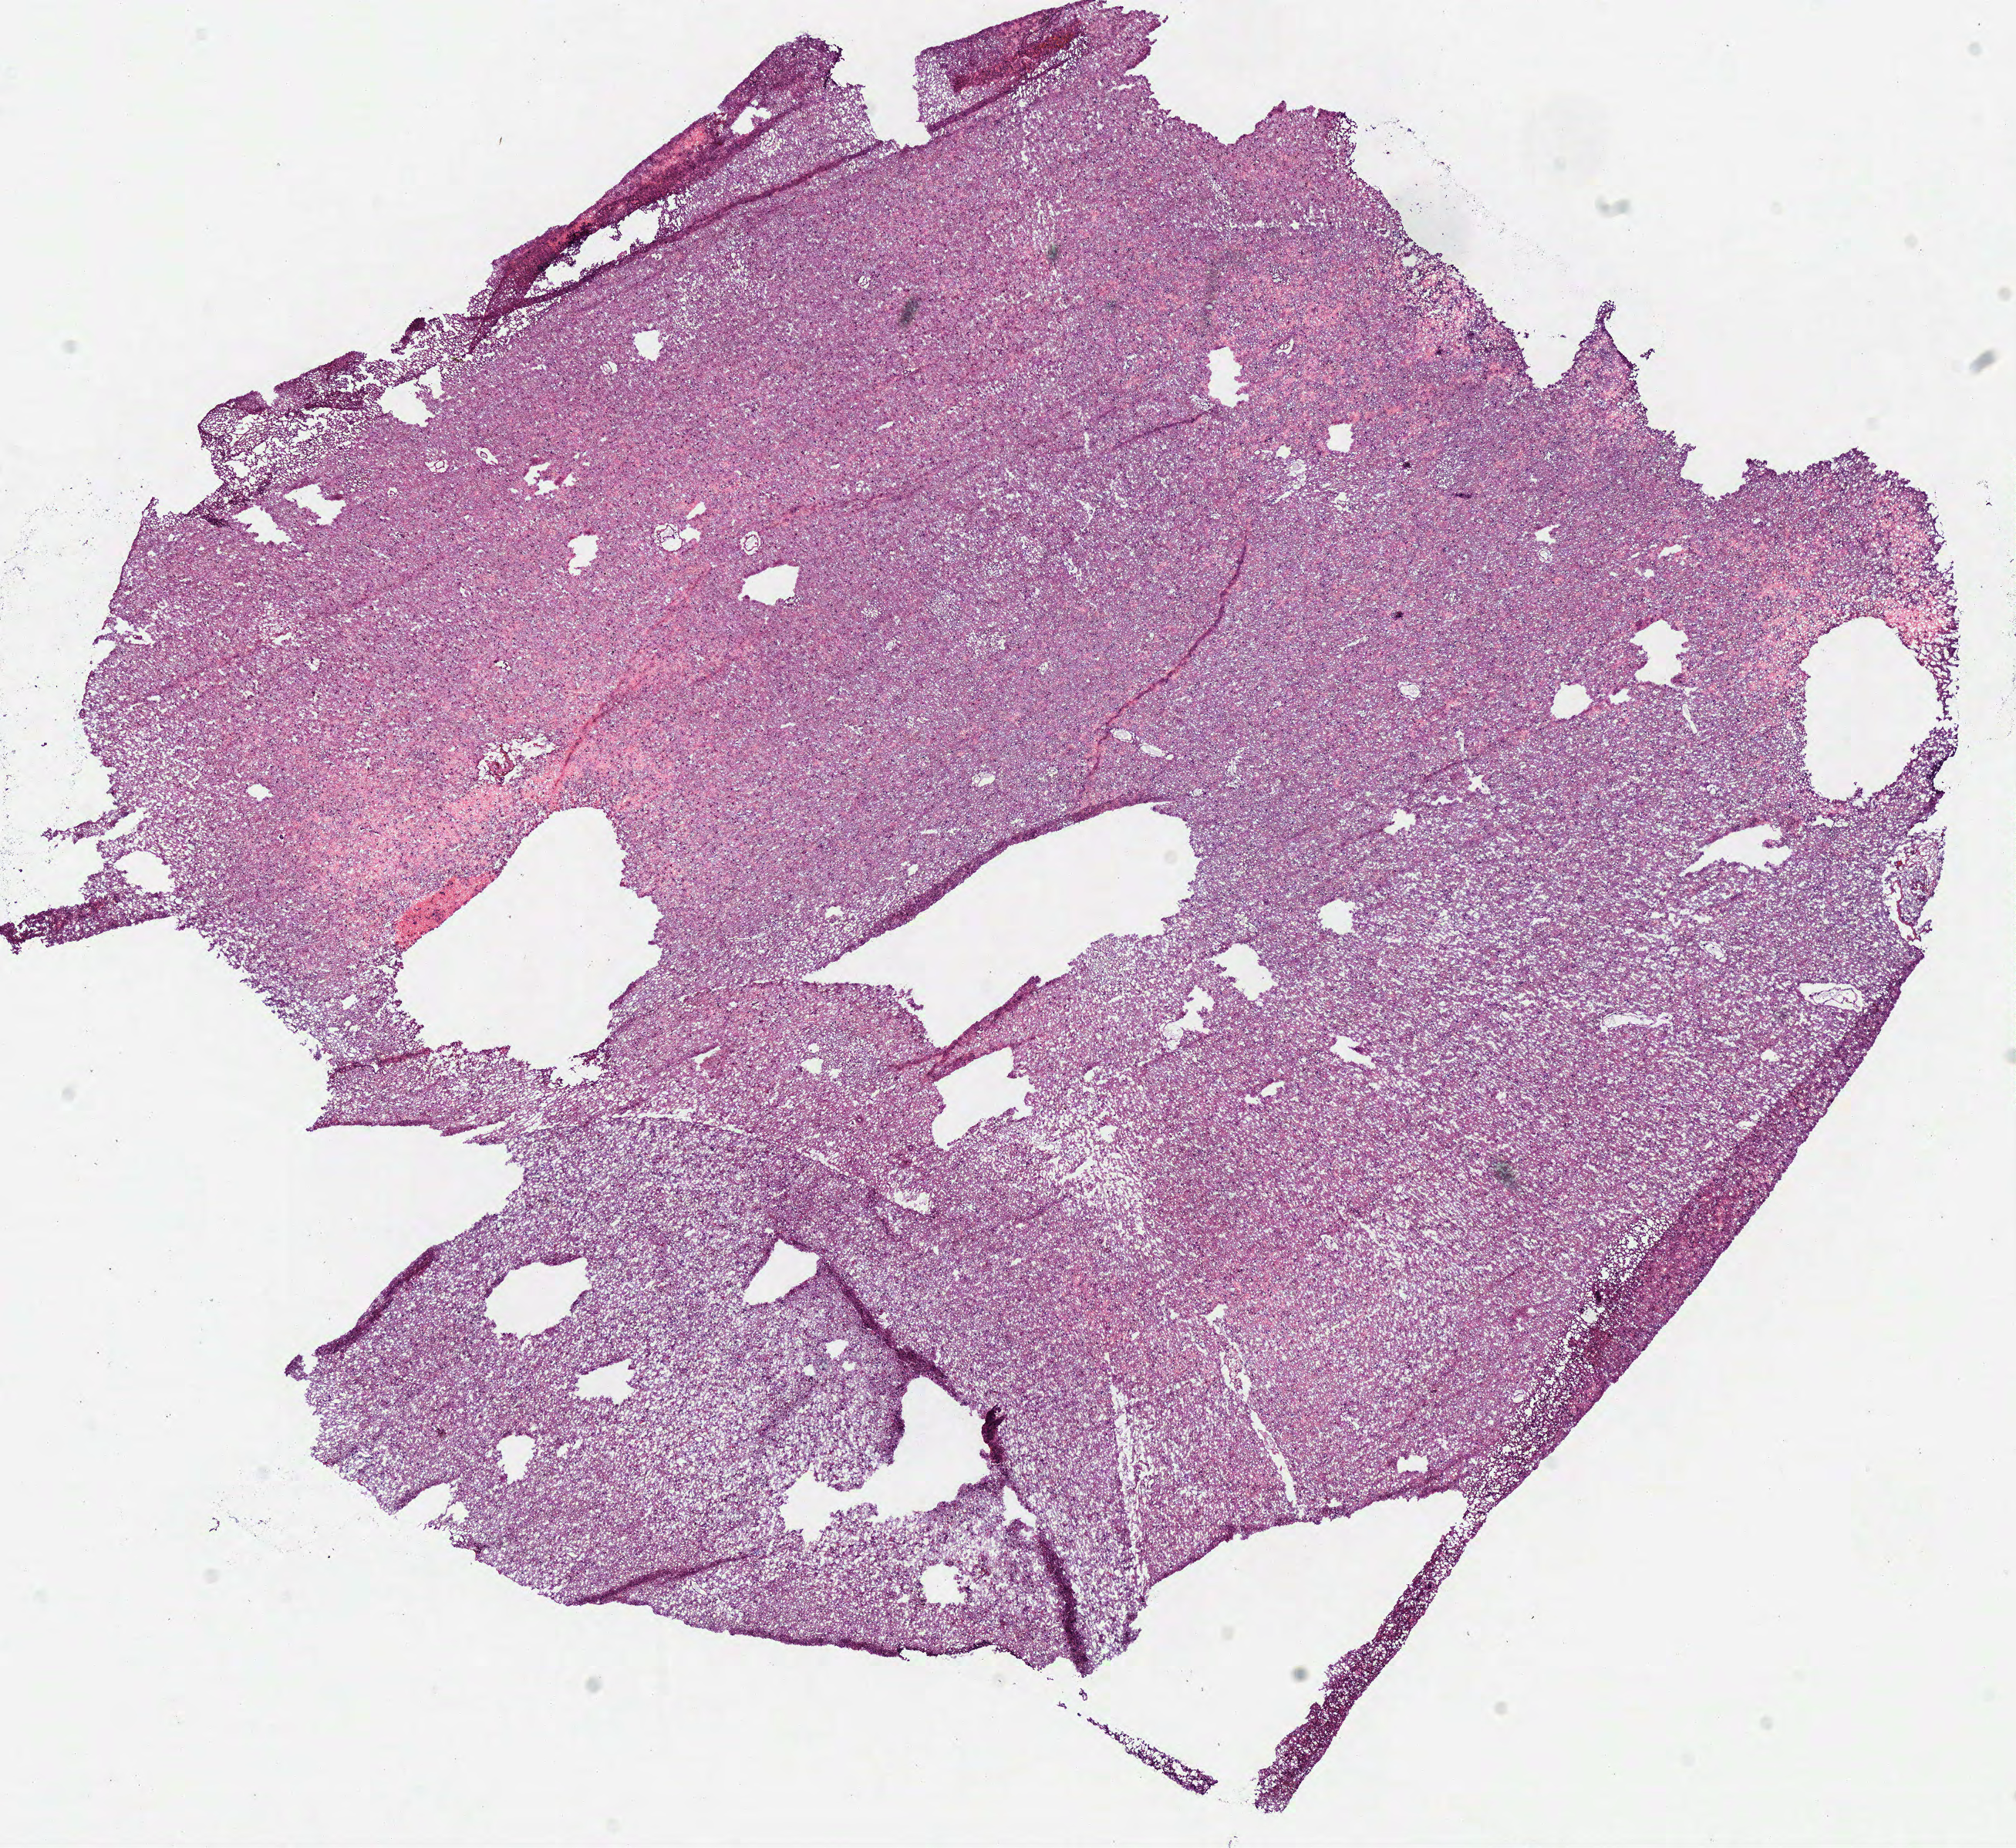
Digitized H&E tissue section (whole slide) — shown as a low-resolution overview of the whole scanned area (about 10.3 x 9.4 mm, from a 40x scan); frozen section; sample: primary tumour, brain. Female, age 59 years at initial diagnosis. Histologic grade: G3 (poorly differentiated). Pathologist review of this section (percent, as recorded): tumour cells 100%, tumour nuclei 65%, normal cells 0%, stromal cells 0%, necrosis 0%.
- diagnosis: Astrocytoma, anaplastic